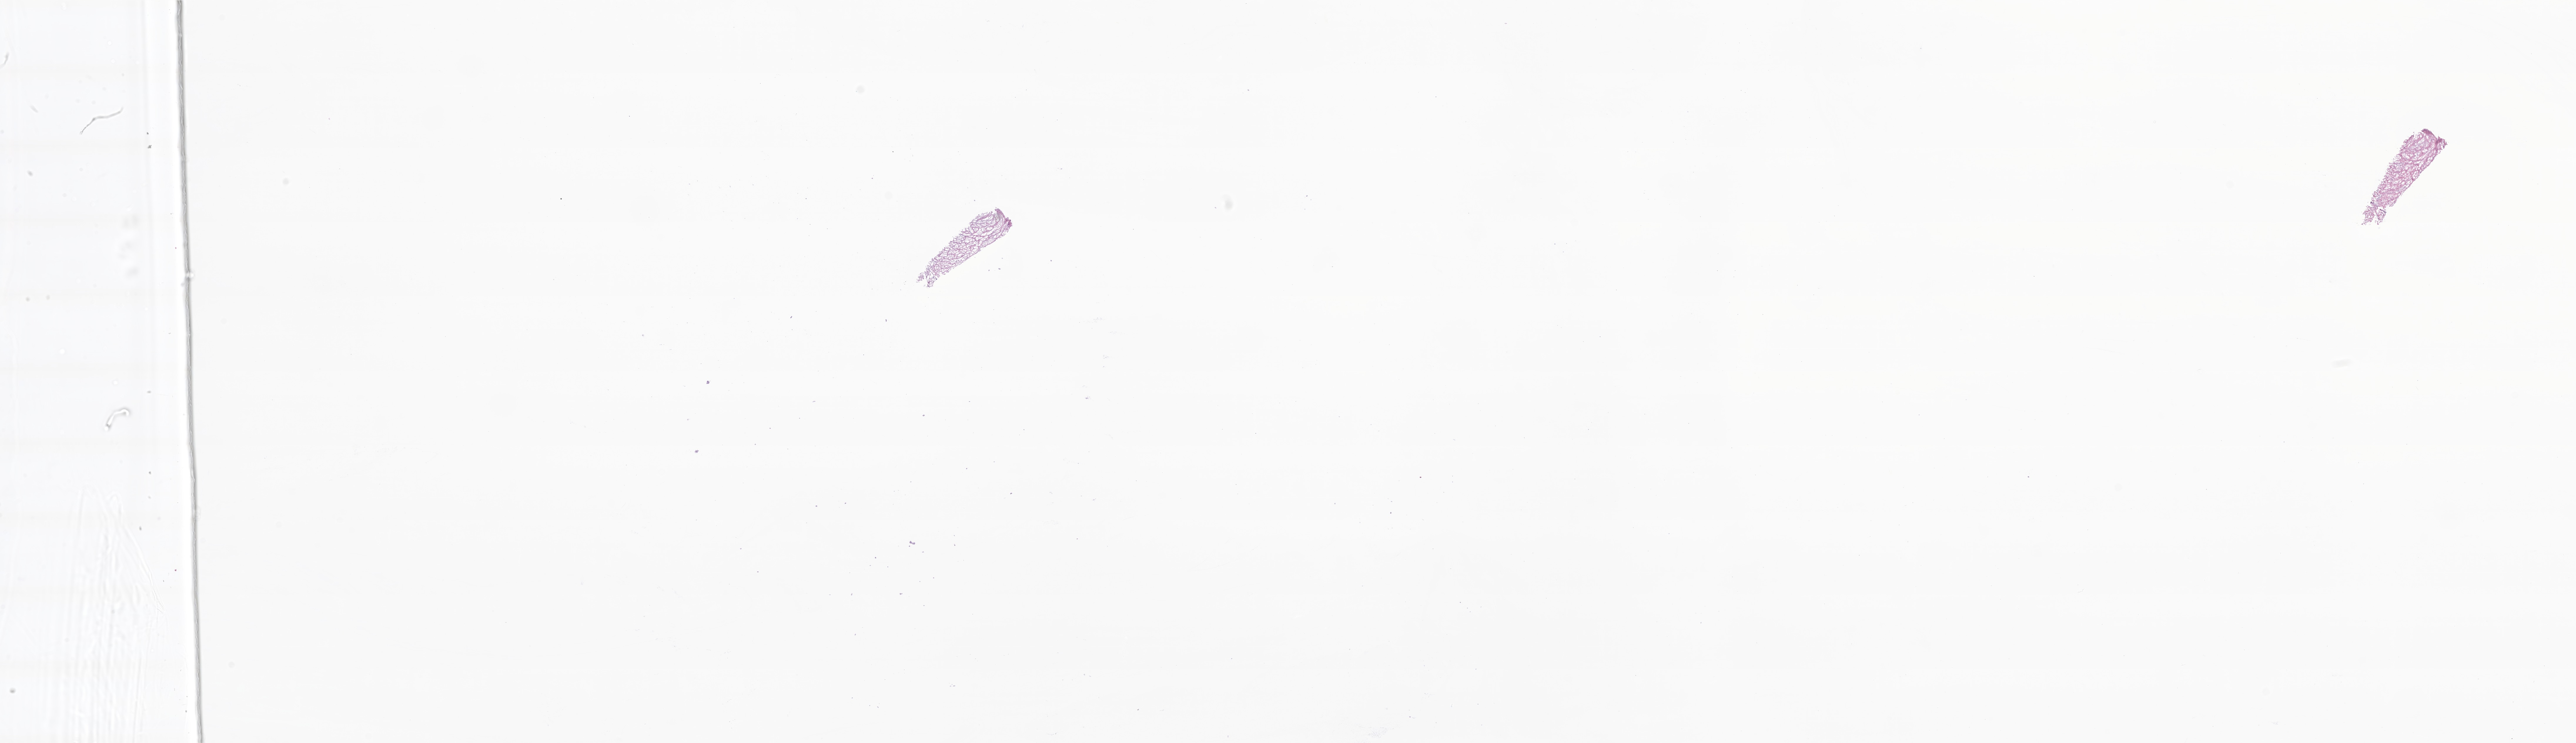
Digitized H&E-stained section of tumor tissue from the soft tissue of trunk — low-resolution overview of the scanned area, about 36.9 x 10.7 mm. Cryosection (OCT / tissue freezing medium). Patient: male, age 120 months.
* tissue or organ of origin (case record): connective, subcutaneous and other soft tissues of trunk
* recorded diagnosis: Aggressive fibromatosis